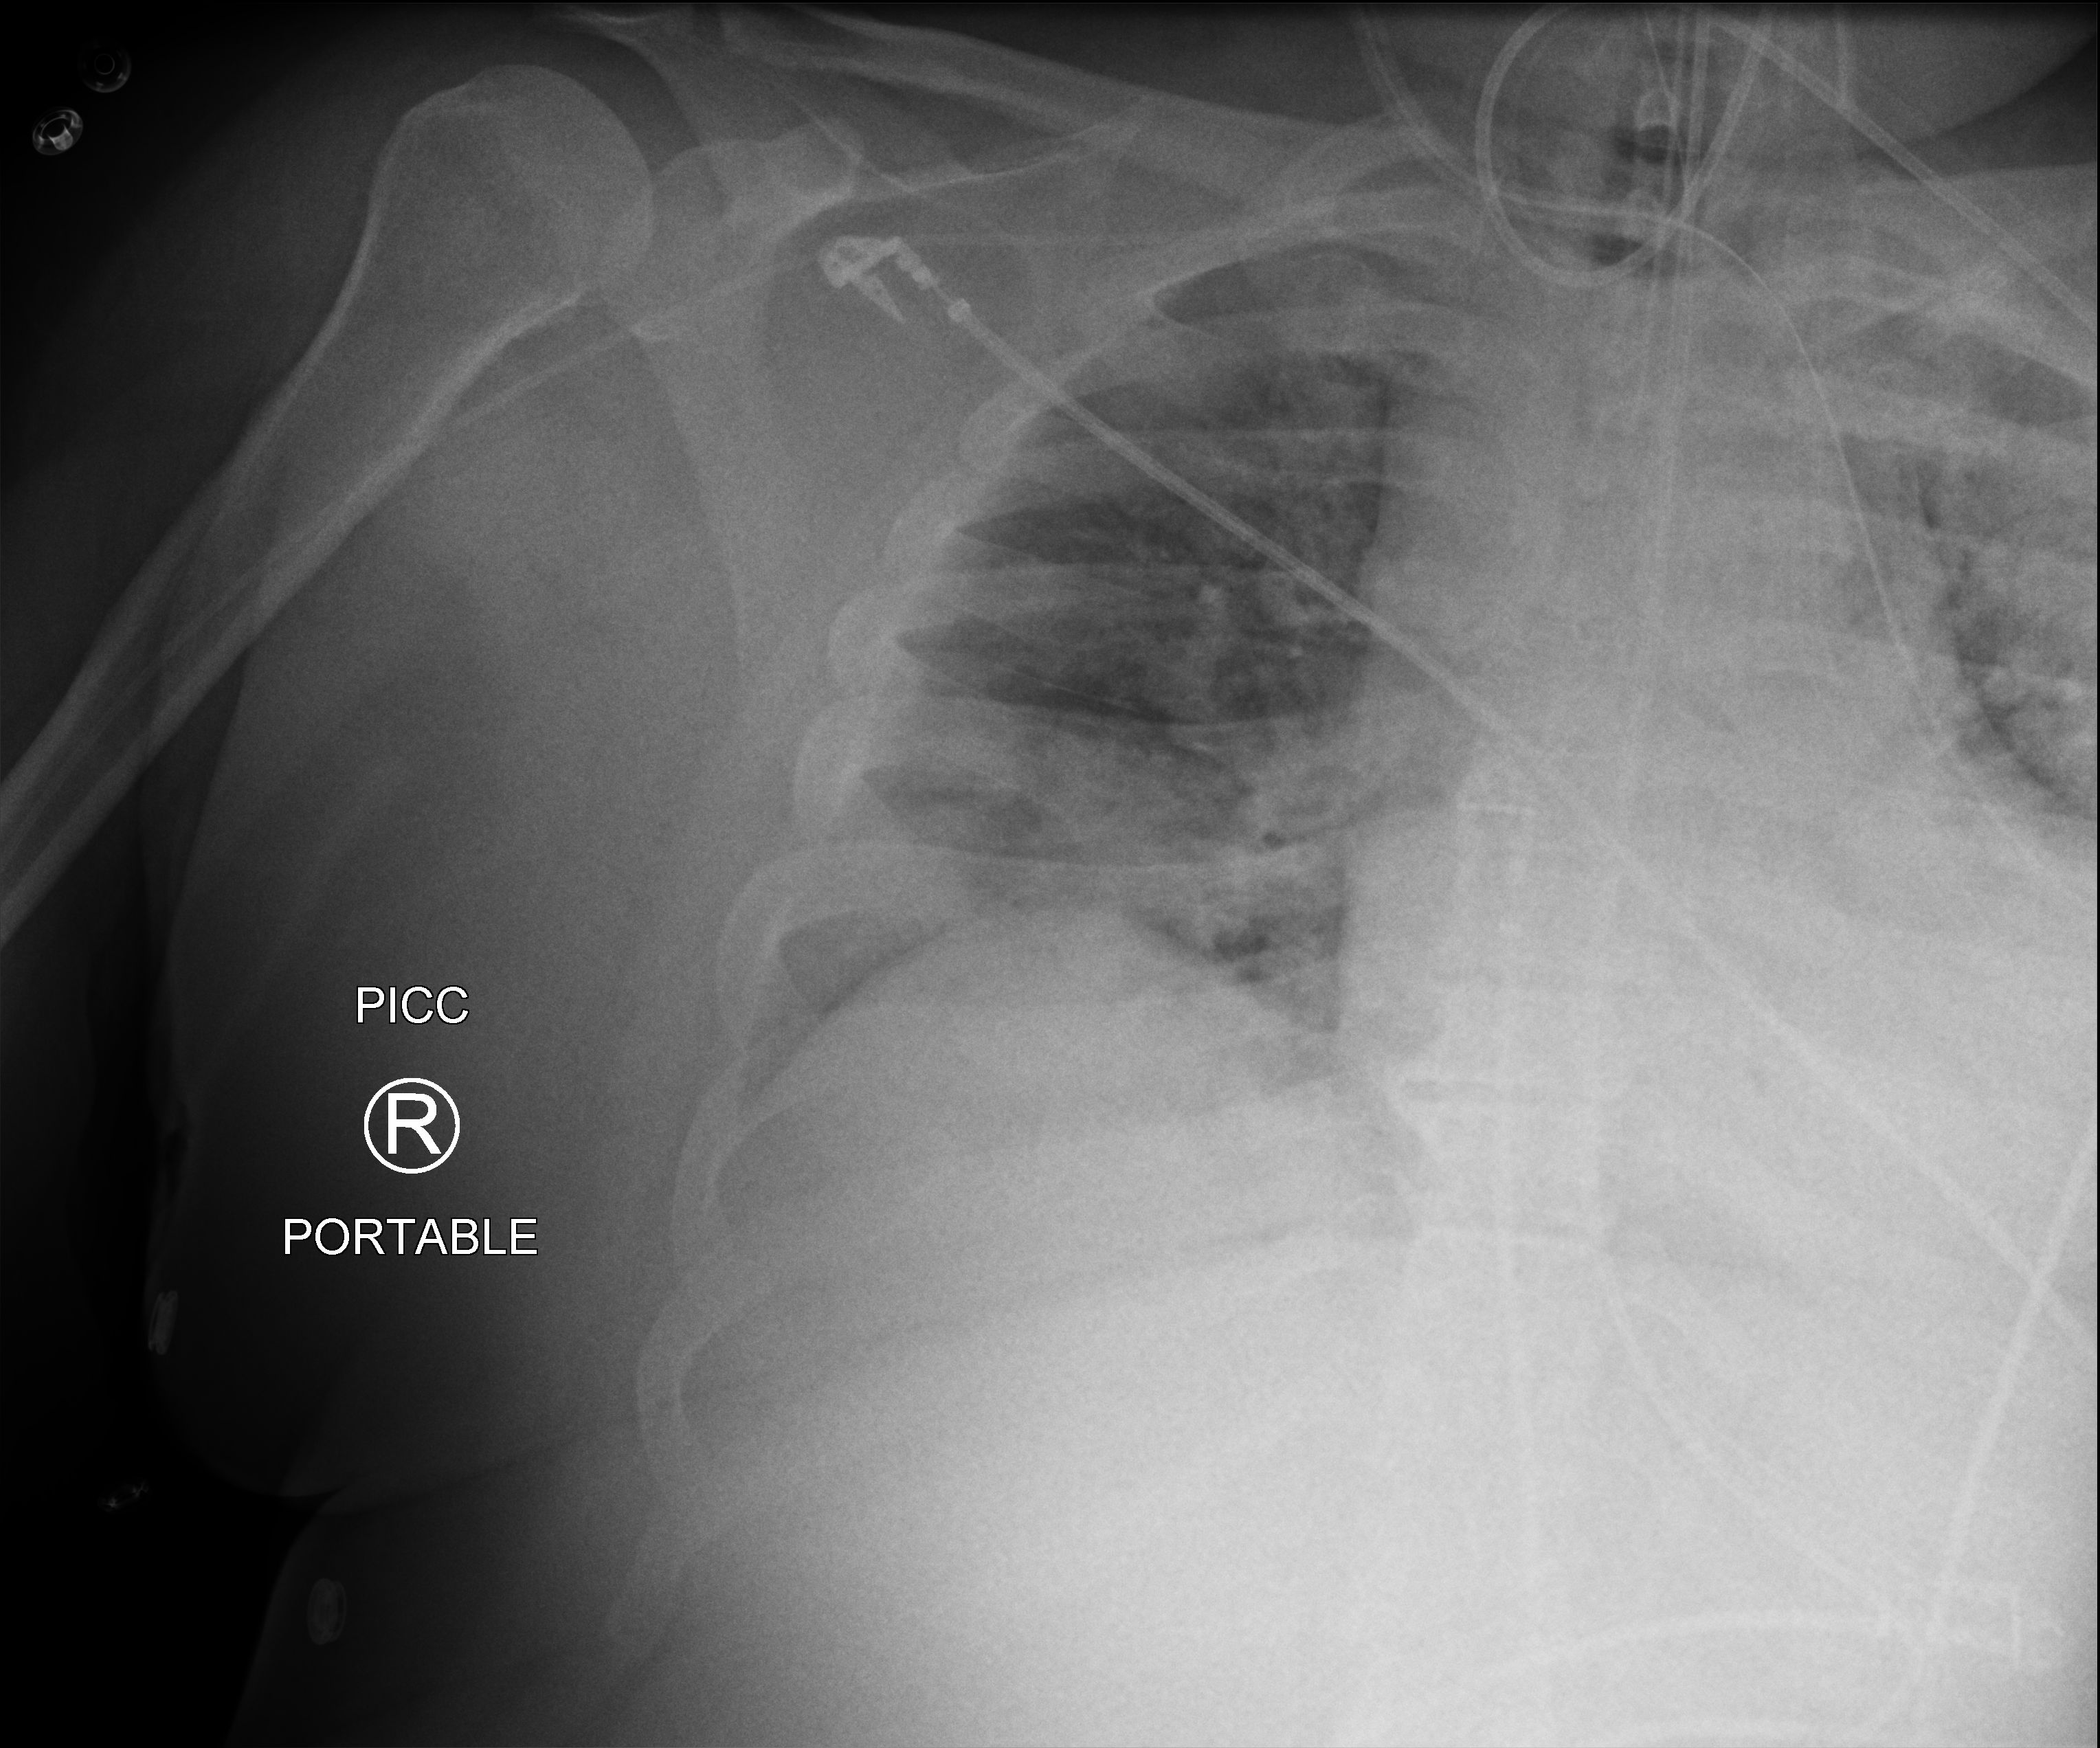
Portable chest radiograph; anteroposterior (AP) projection. Patient hospitalised with COVID-19, aged 18–59 years.
From the hospital-stay record, not from the radiograph (when in the stay this image was taken is not recorded): mechanically ventilated during this hospital stay: yes; admitted to intensive care during this hospital stay: yes; length of hospital stay: 10 days.